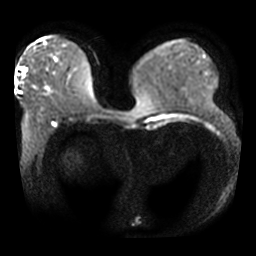
Breast MRI, one axial slice; slice 13 of 42 in the series (ordered by position); diffusion-weighted series; image 2 of 4 stored at this slice position (different b-values; order by instance number); 3 T; 256 × 256 image matrix, field of view 360 × 360 mm. Female patient.
Annotated regions visible in this slice (expert manual segmentation):
- tumour on diffusion-weighted imaging: box from (x=23, y=68) to (x=26, y=72) px